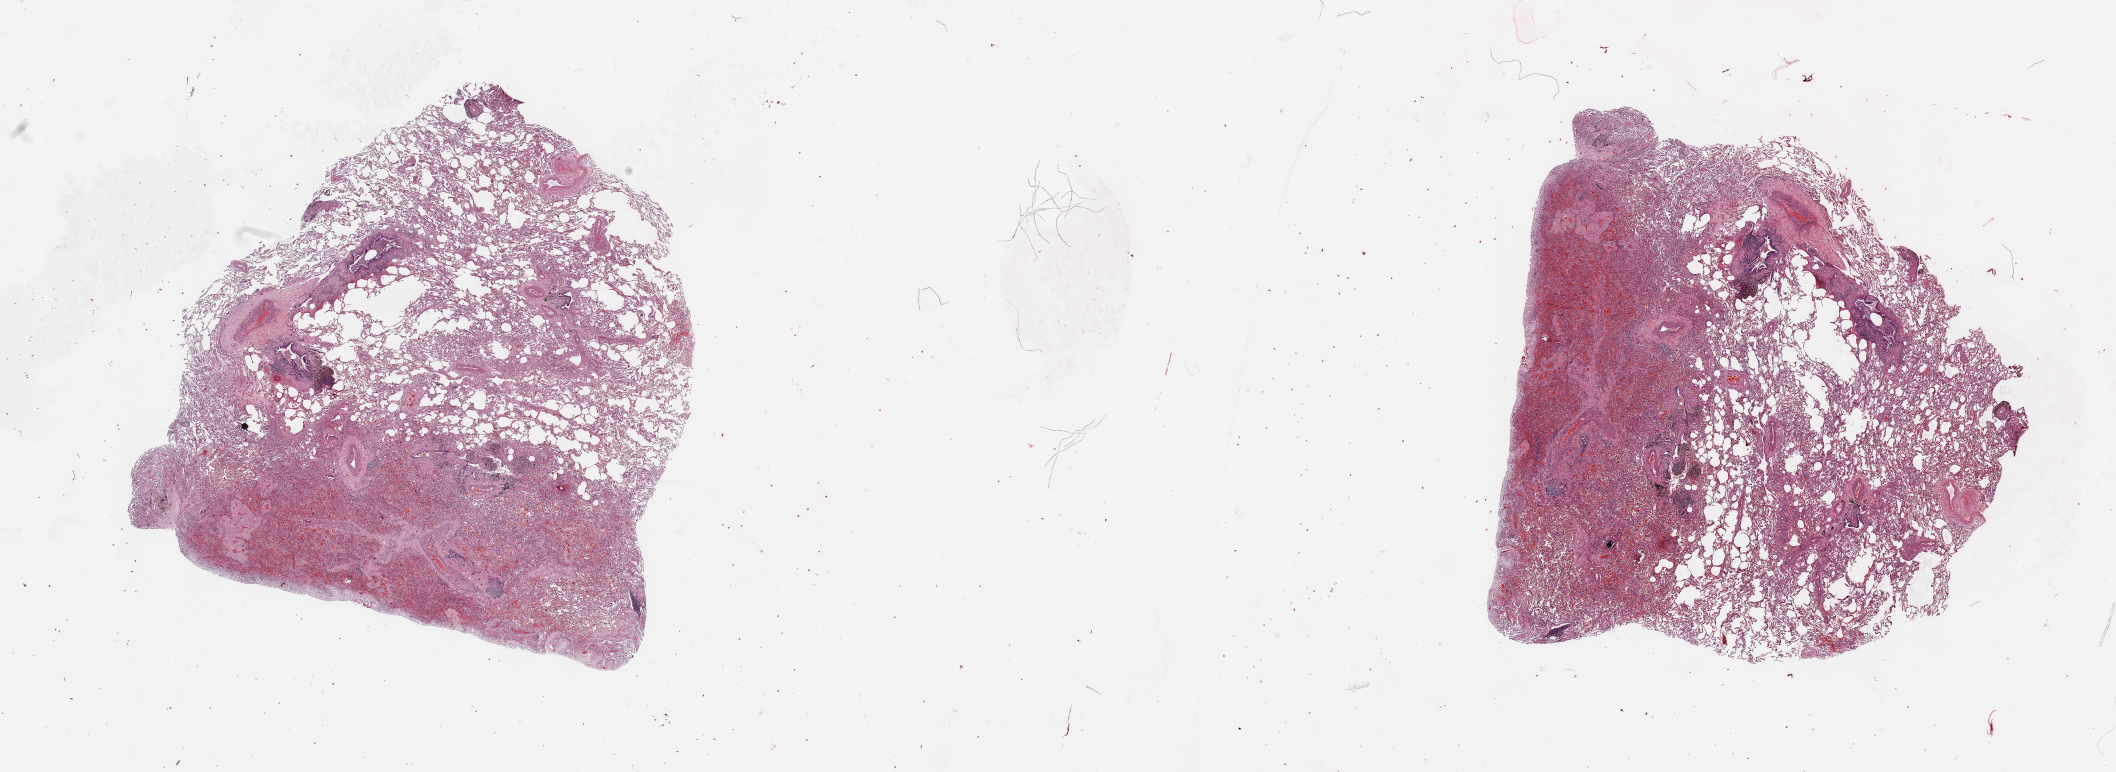
H&E-stained whole-slide image — whole scanned area (about 33.5 x 12.2 mm, slide scanned at 20x) shown as a low-resolution overview; lung, normal (non-tumour) tissue. Patient: male, age 66 years.
This section: normal (non-tumour) tissue from the same patient. Patient diagnosis: Squamous cell carcinoma, NOS.